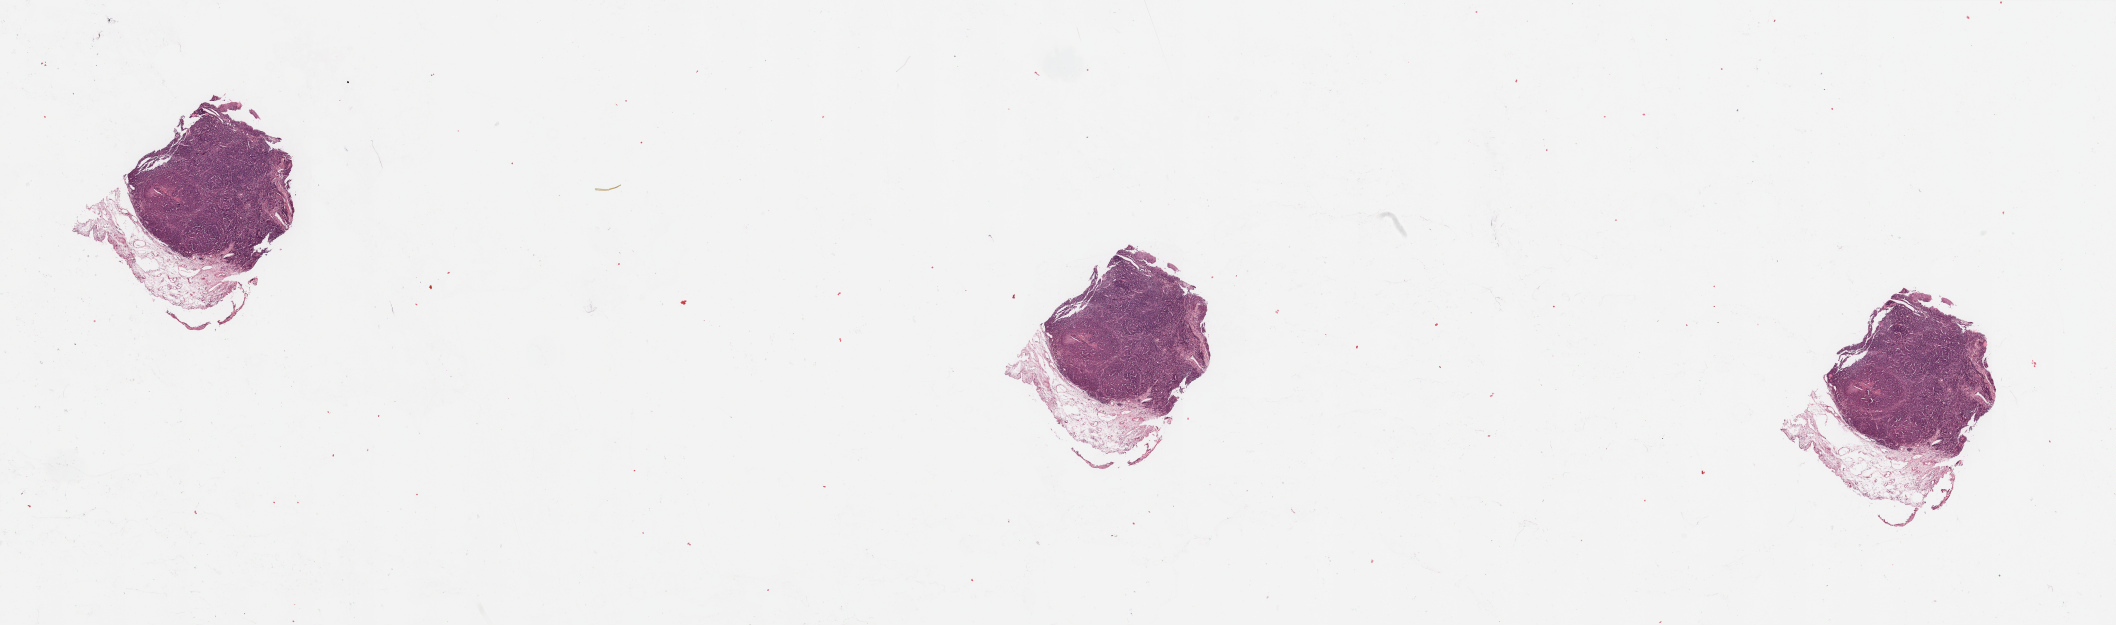
Whole-slide histology image, H&E, a low-resolution overview of the entire scanned area, about 33.5 x 9.9 mm, head and neck, tissue type not recorded. Patient: male, age 67 years.
- patient diagnosis: Squamous cell carcinoma, NOS (gum, NOS)